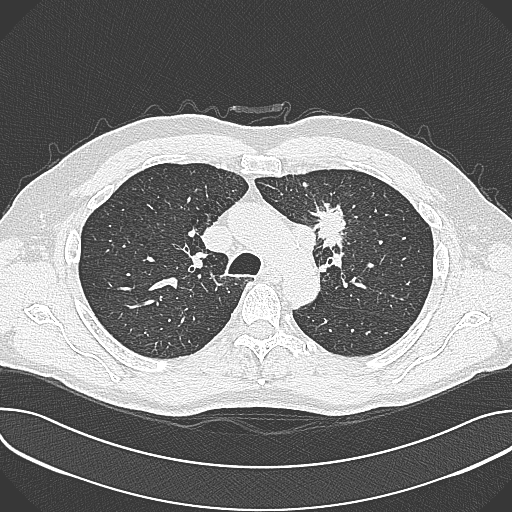
Chest CT (low-dose screening protocol), one axial image; first (baseline) screen; lung window (W 1500 / L -600 HU); 1 mm slice thickness; slice 99 of 361 in the series. Male participant, aged 59 years at enrolment.
• Lesion marked by an expert reader, bounding box (x1, y1, x2, y2) in pixels: (302, 198, 360, 257).
• The screening reader recorded 2 non-calcified nodules or masses ≥4 mm on this exam (left upper lobe, left upper lobe); which of them this box marks is not recorded.
• Participant outcome: lung cancer diagnosed 21 days after this screen — non-small cell carcinoma, left upper lobe, poorly differentiated (G3), stage IIIA (AJCC 6th edition), 35 mm at pathology.